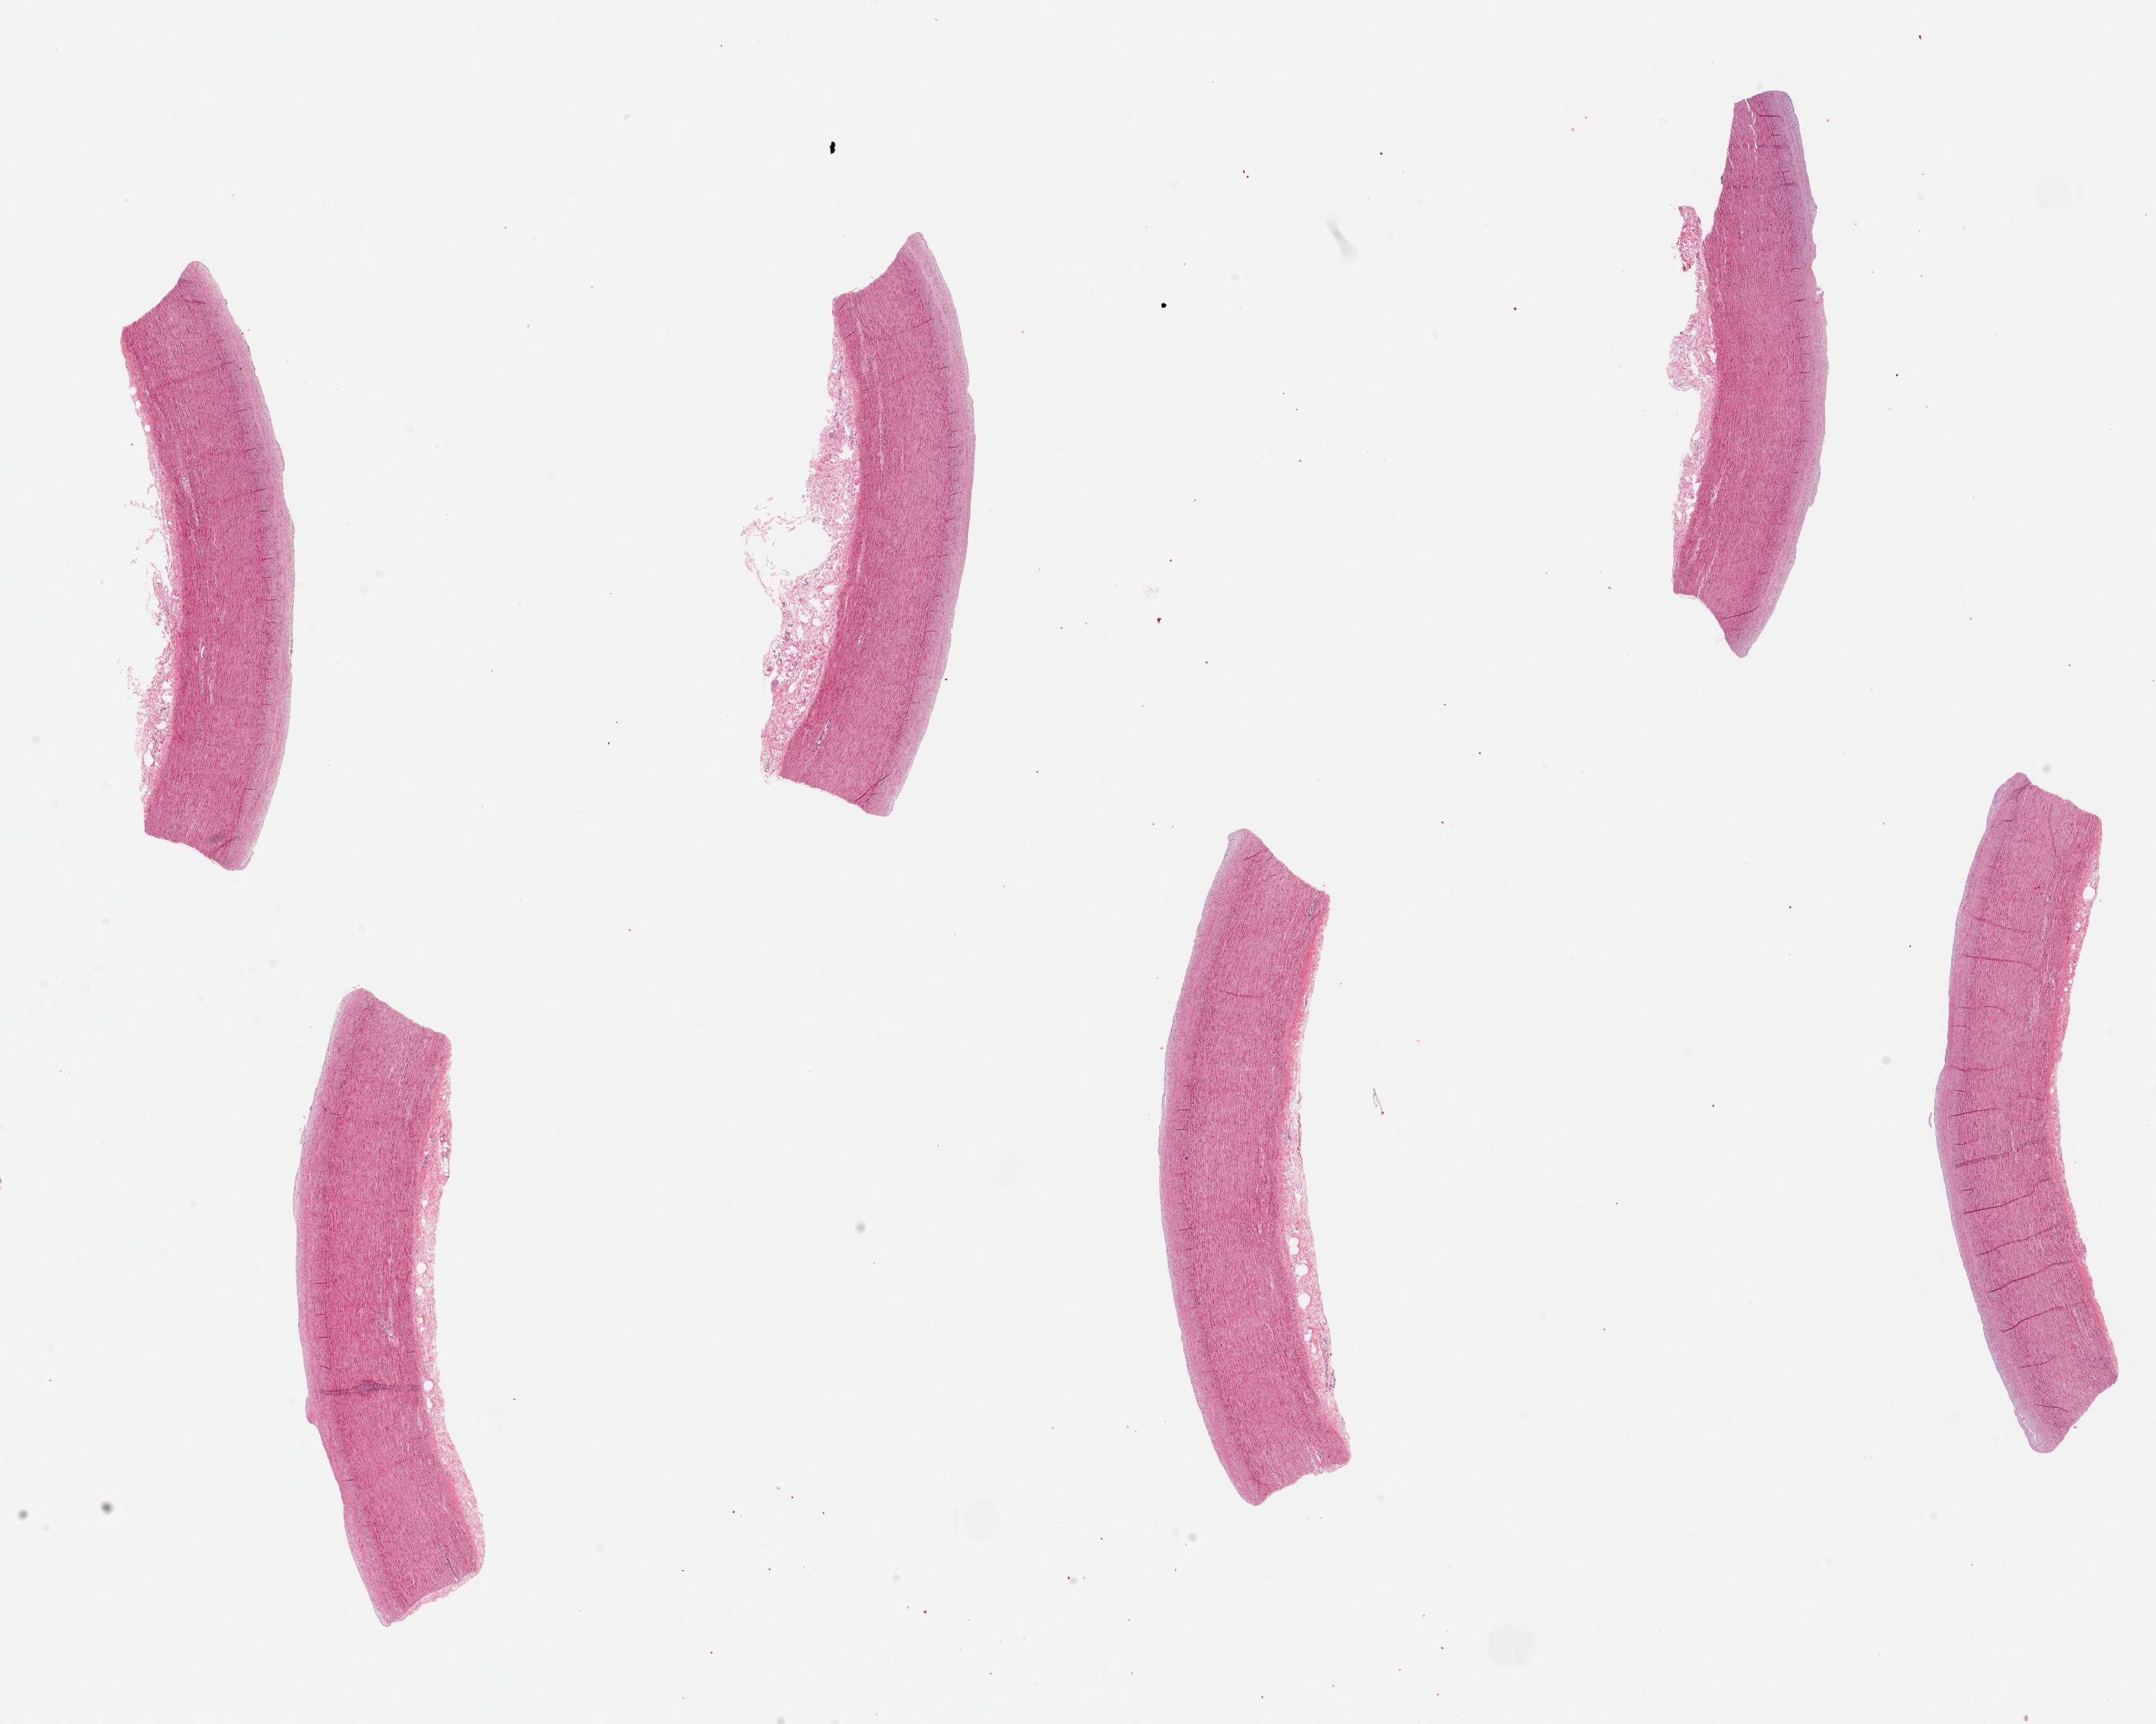
Digitized H&E-stained section — a low-resolution overview of the entire scanned area, about 26.6 x 21.2 mm. PAXgene-fixed, paraffin-embedded tissue. Target tissue: aorta. Tissue donor sample. Donor: male.
Review note (as recorded): 6 pieces, up to 8x2mm.